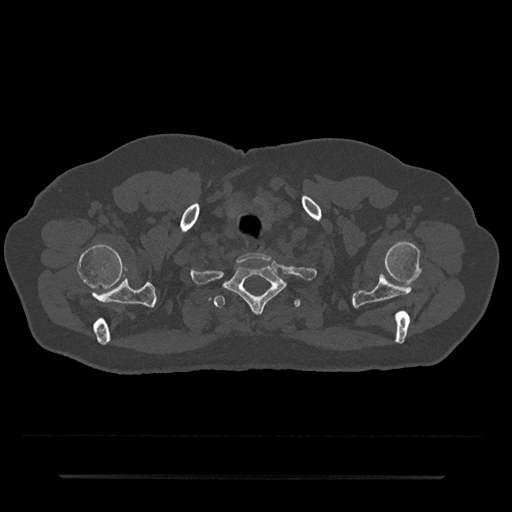
CT including the spine, one axial slice. Slice 638 of 797 in the series (ordered by position). Bone window (W 1800 / L 400 HU). 0.5 mm slice thickness. 512 × 512 image matrix, field of view 437 × 437 mm. Male patient, age 69 years. Case-level facts recorded for this patient, not image findings: primary cancer: prostate.
Outlined on this slice (semi-automatic segmentation, software-assisted and operator-edited):
- T1 vertebra: bounding box [x1, y1, x2, y2] px = [225, 262, 285, 313]
- T2 vertebra: [214, 295, 301, 308]